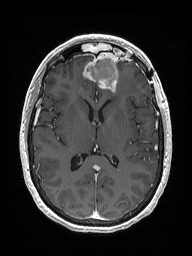
Brain MRI from a brain-tumour surgery series, one axial slice. Position 81 of 192 along the scan axis. T1-weighted post-contrast. 192 × 256 image matrix, field of view 187 × 250 mm. Case-level facts recorded for this patient, not image findings: histopathology: Metastastic Carcinoma from Breast primary; tumour location: Right Frontal.
Structures marked on this image (manually delineated by an expert):
- previous resection cavity: box from (x=85, y=52) to (x=118, y=82) px